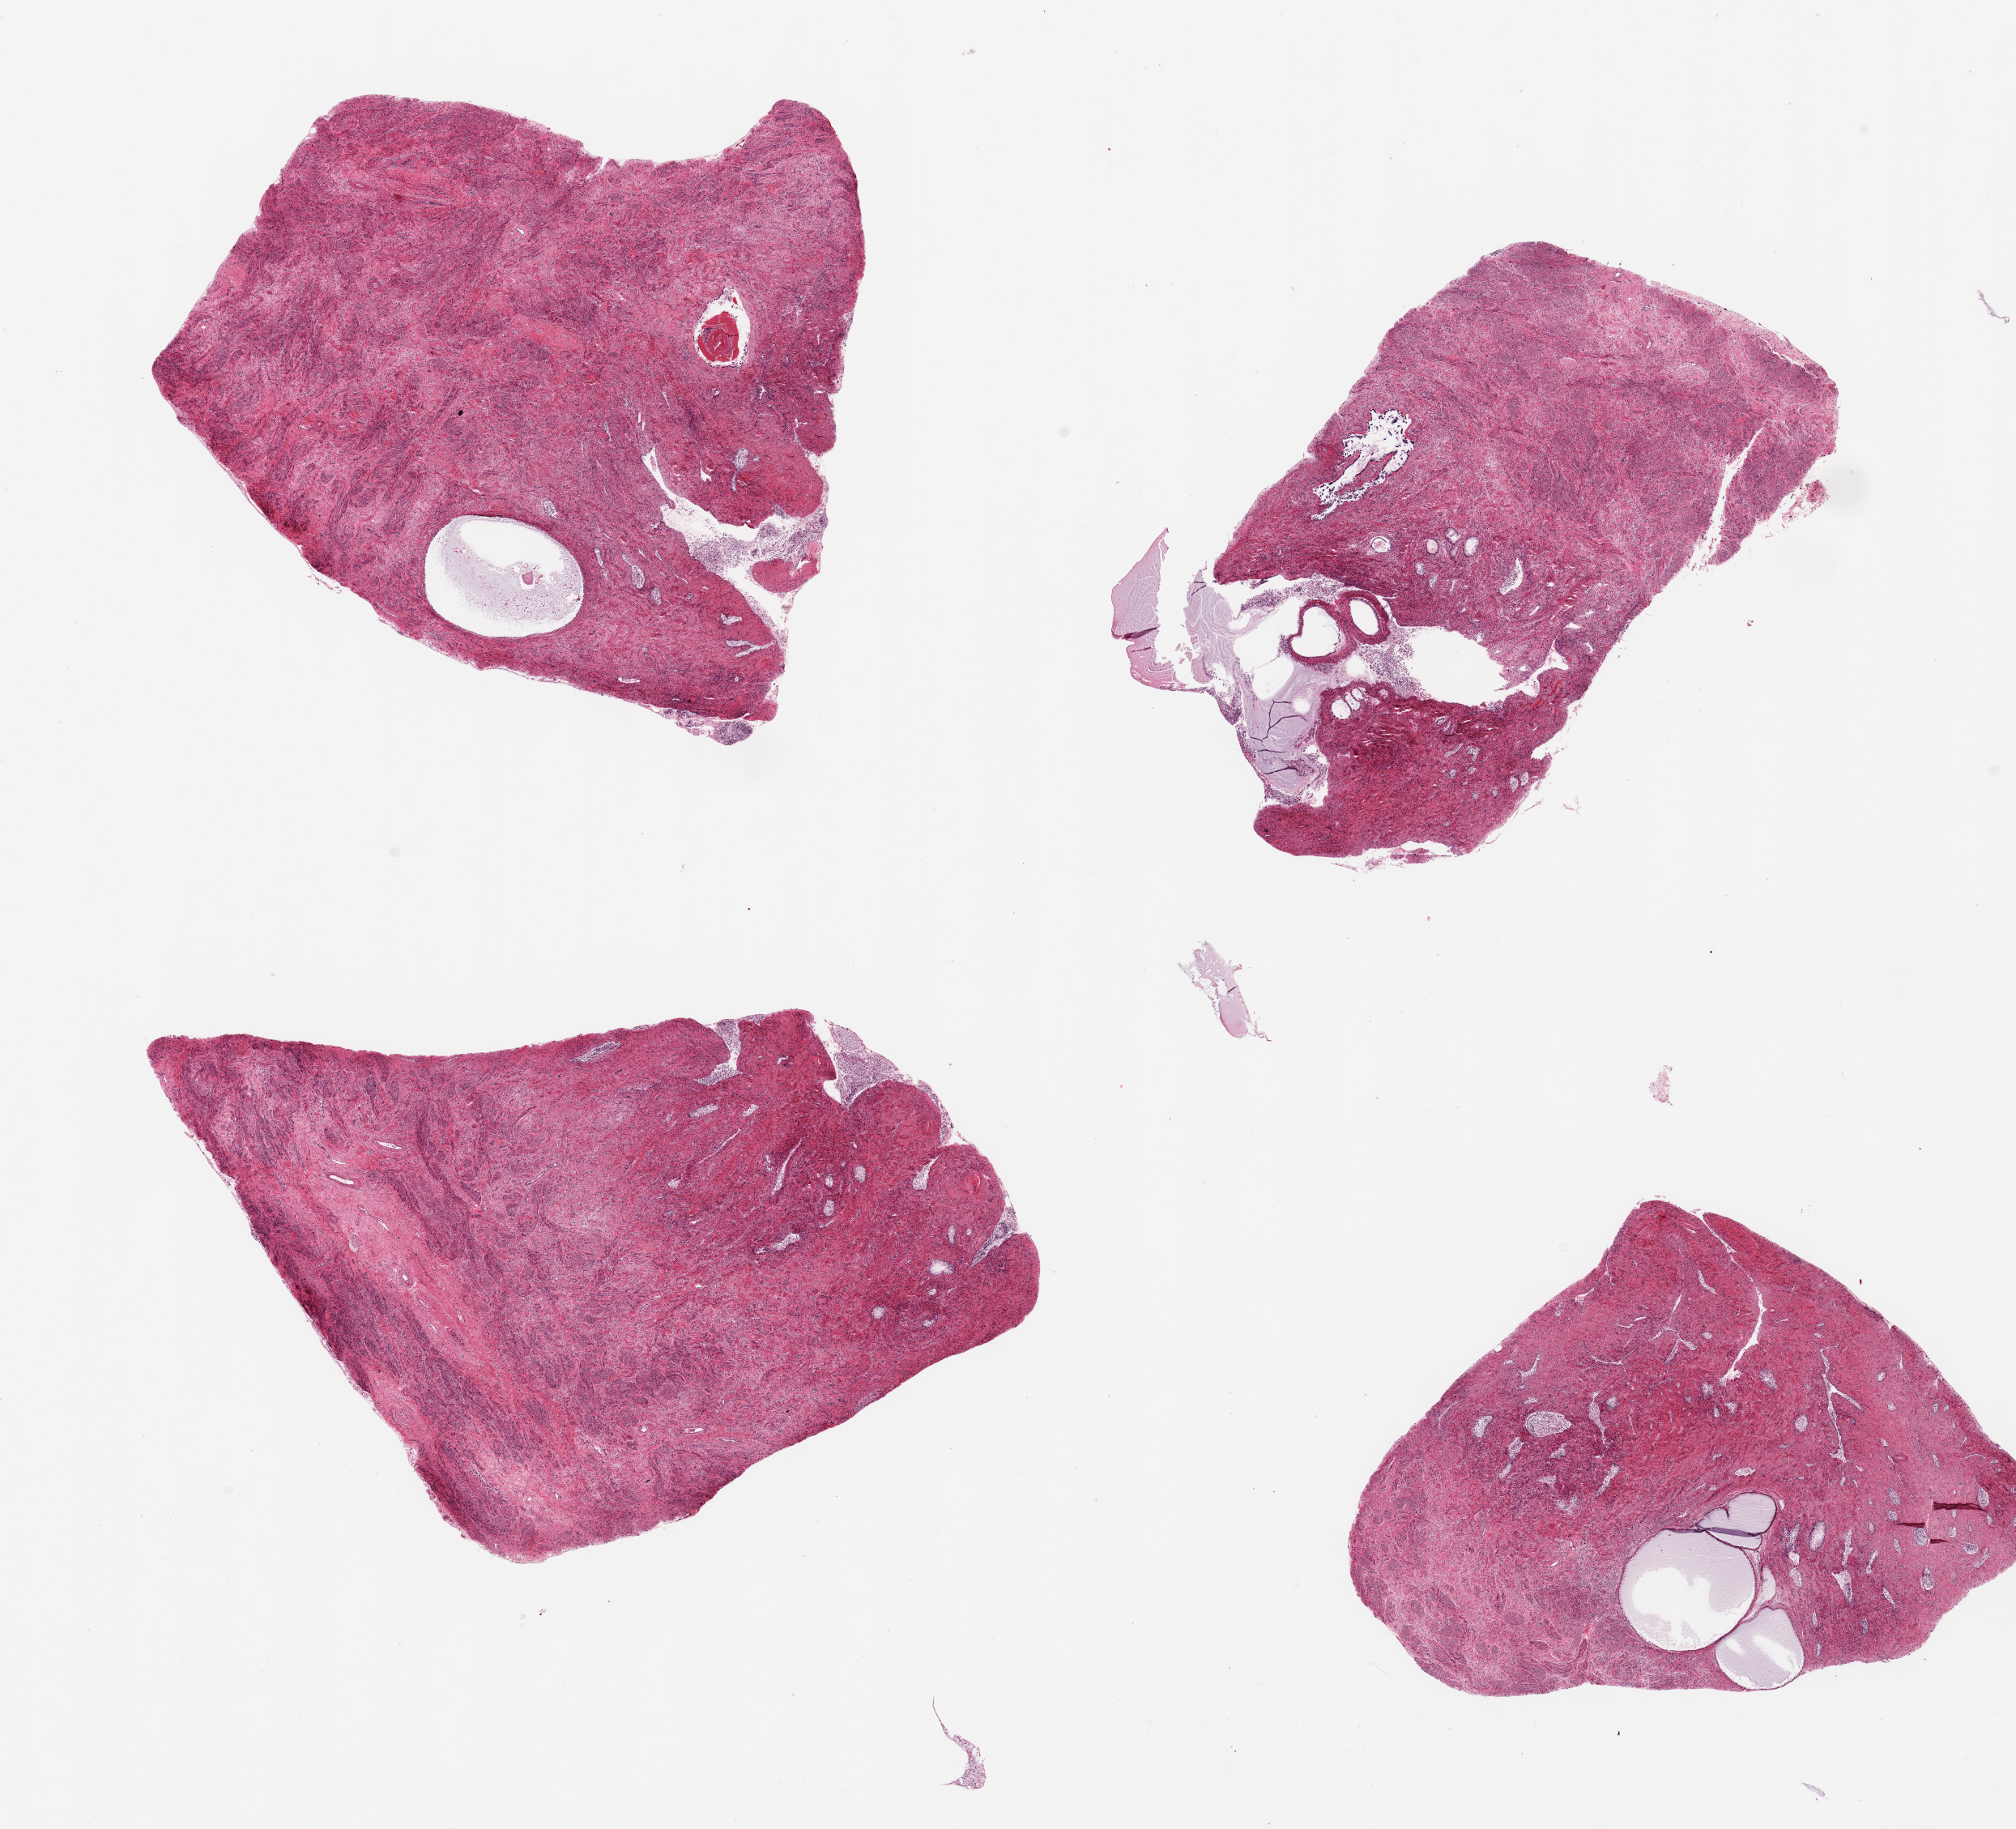
Whole-slide image, haematoxylin and eosin stain, shown as a low-resolution overview of the whole scanned area (about 19.7 x 17.9 mm), PAXgene-fixed paraffin-embedded (PFPE) section, sampled site (target tissue): endocervix, donor tissue sample.
- reviewer comment on this tissue sample: 4 aliquots ~6x5mm. Mucosa badly autolyzed